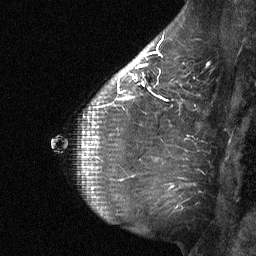
Breast MRI (dynamic contrast-enhanced), one sagittal slice. Position 45 of 64 along the scan axis. Dynamic contrast-enhanced study with each time point stored as its own series, time point 2 of 3 at this slice position (early post-contrast, ordered by acquisition time). 1.5 T. TE 4.8 ms, TR 27 ms. 2 mm slice thickness. 256 × 256 image matrix. Patient: female, 51 years. From the clinical record (not read from this slice): setting: breast cancer imaged before/during neoadjuvant chemotherapy; receptor status: HR-positive, HER2-negative.
Annotated regions visible in this slice (semi-automatically segmented with operator editing):
- analysis volume of interest (the breast-tissue region the enhancement analysis was run in; not a lesion): bounding box <112,46,167,106> (left, top, right, bottom; pixels)
- tumour enhancement mask (voxels above the 90 % enhancement threshold inside the analysis volume of interest): <119,51,160,98>